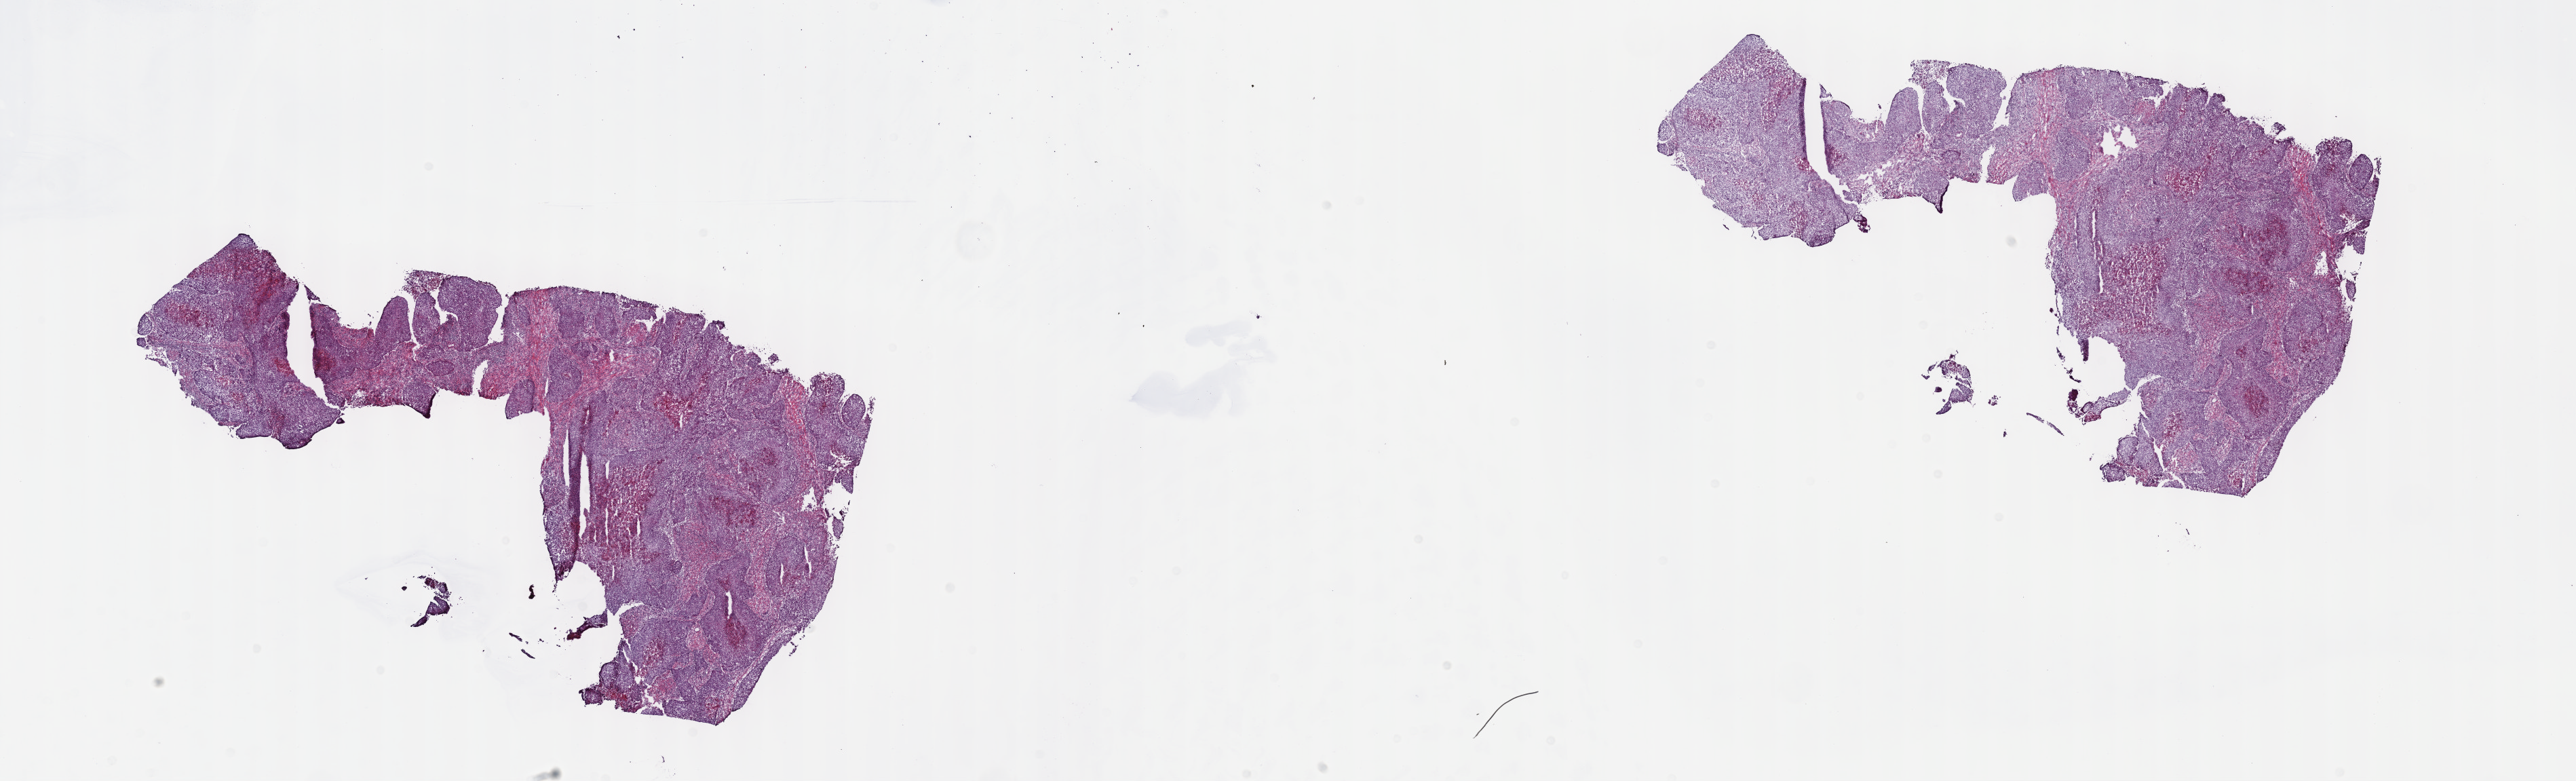
Whole-slide histology image, H&E — shown as a low-resolution overview of the whole scanned area (about 30.7 x 9.3 mm). Frozen section. Primary tumour sample from the bladder. Male, age 47 years at initial diagnosis. Histologic grade: high grade. Slide review estimates, as recorded: tumour cells 96%, tumour nuclei 80%, normal cells 0%, stromal cells 0%, necrosis 4%. Infiltration values recorded for this section: lymphocyte infiltration 2%, monocyte infiltration 0%, neutrophil infiltration 4%.
Histologic diagnosis: Transitional cell carcinoma. Lymph nodes positive (case pathology): 0 of 77 examined. AJCC pathologic stage: III (6th edition).